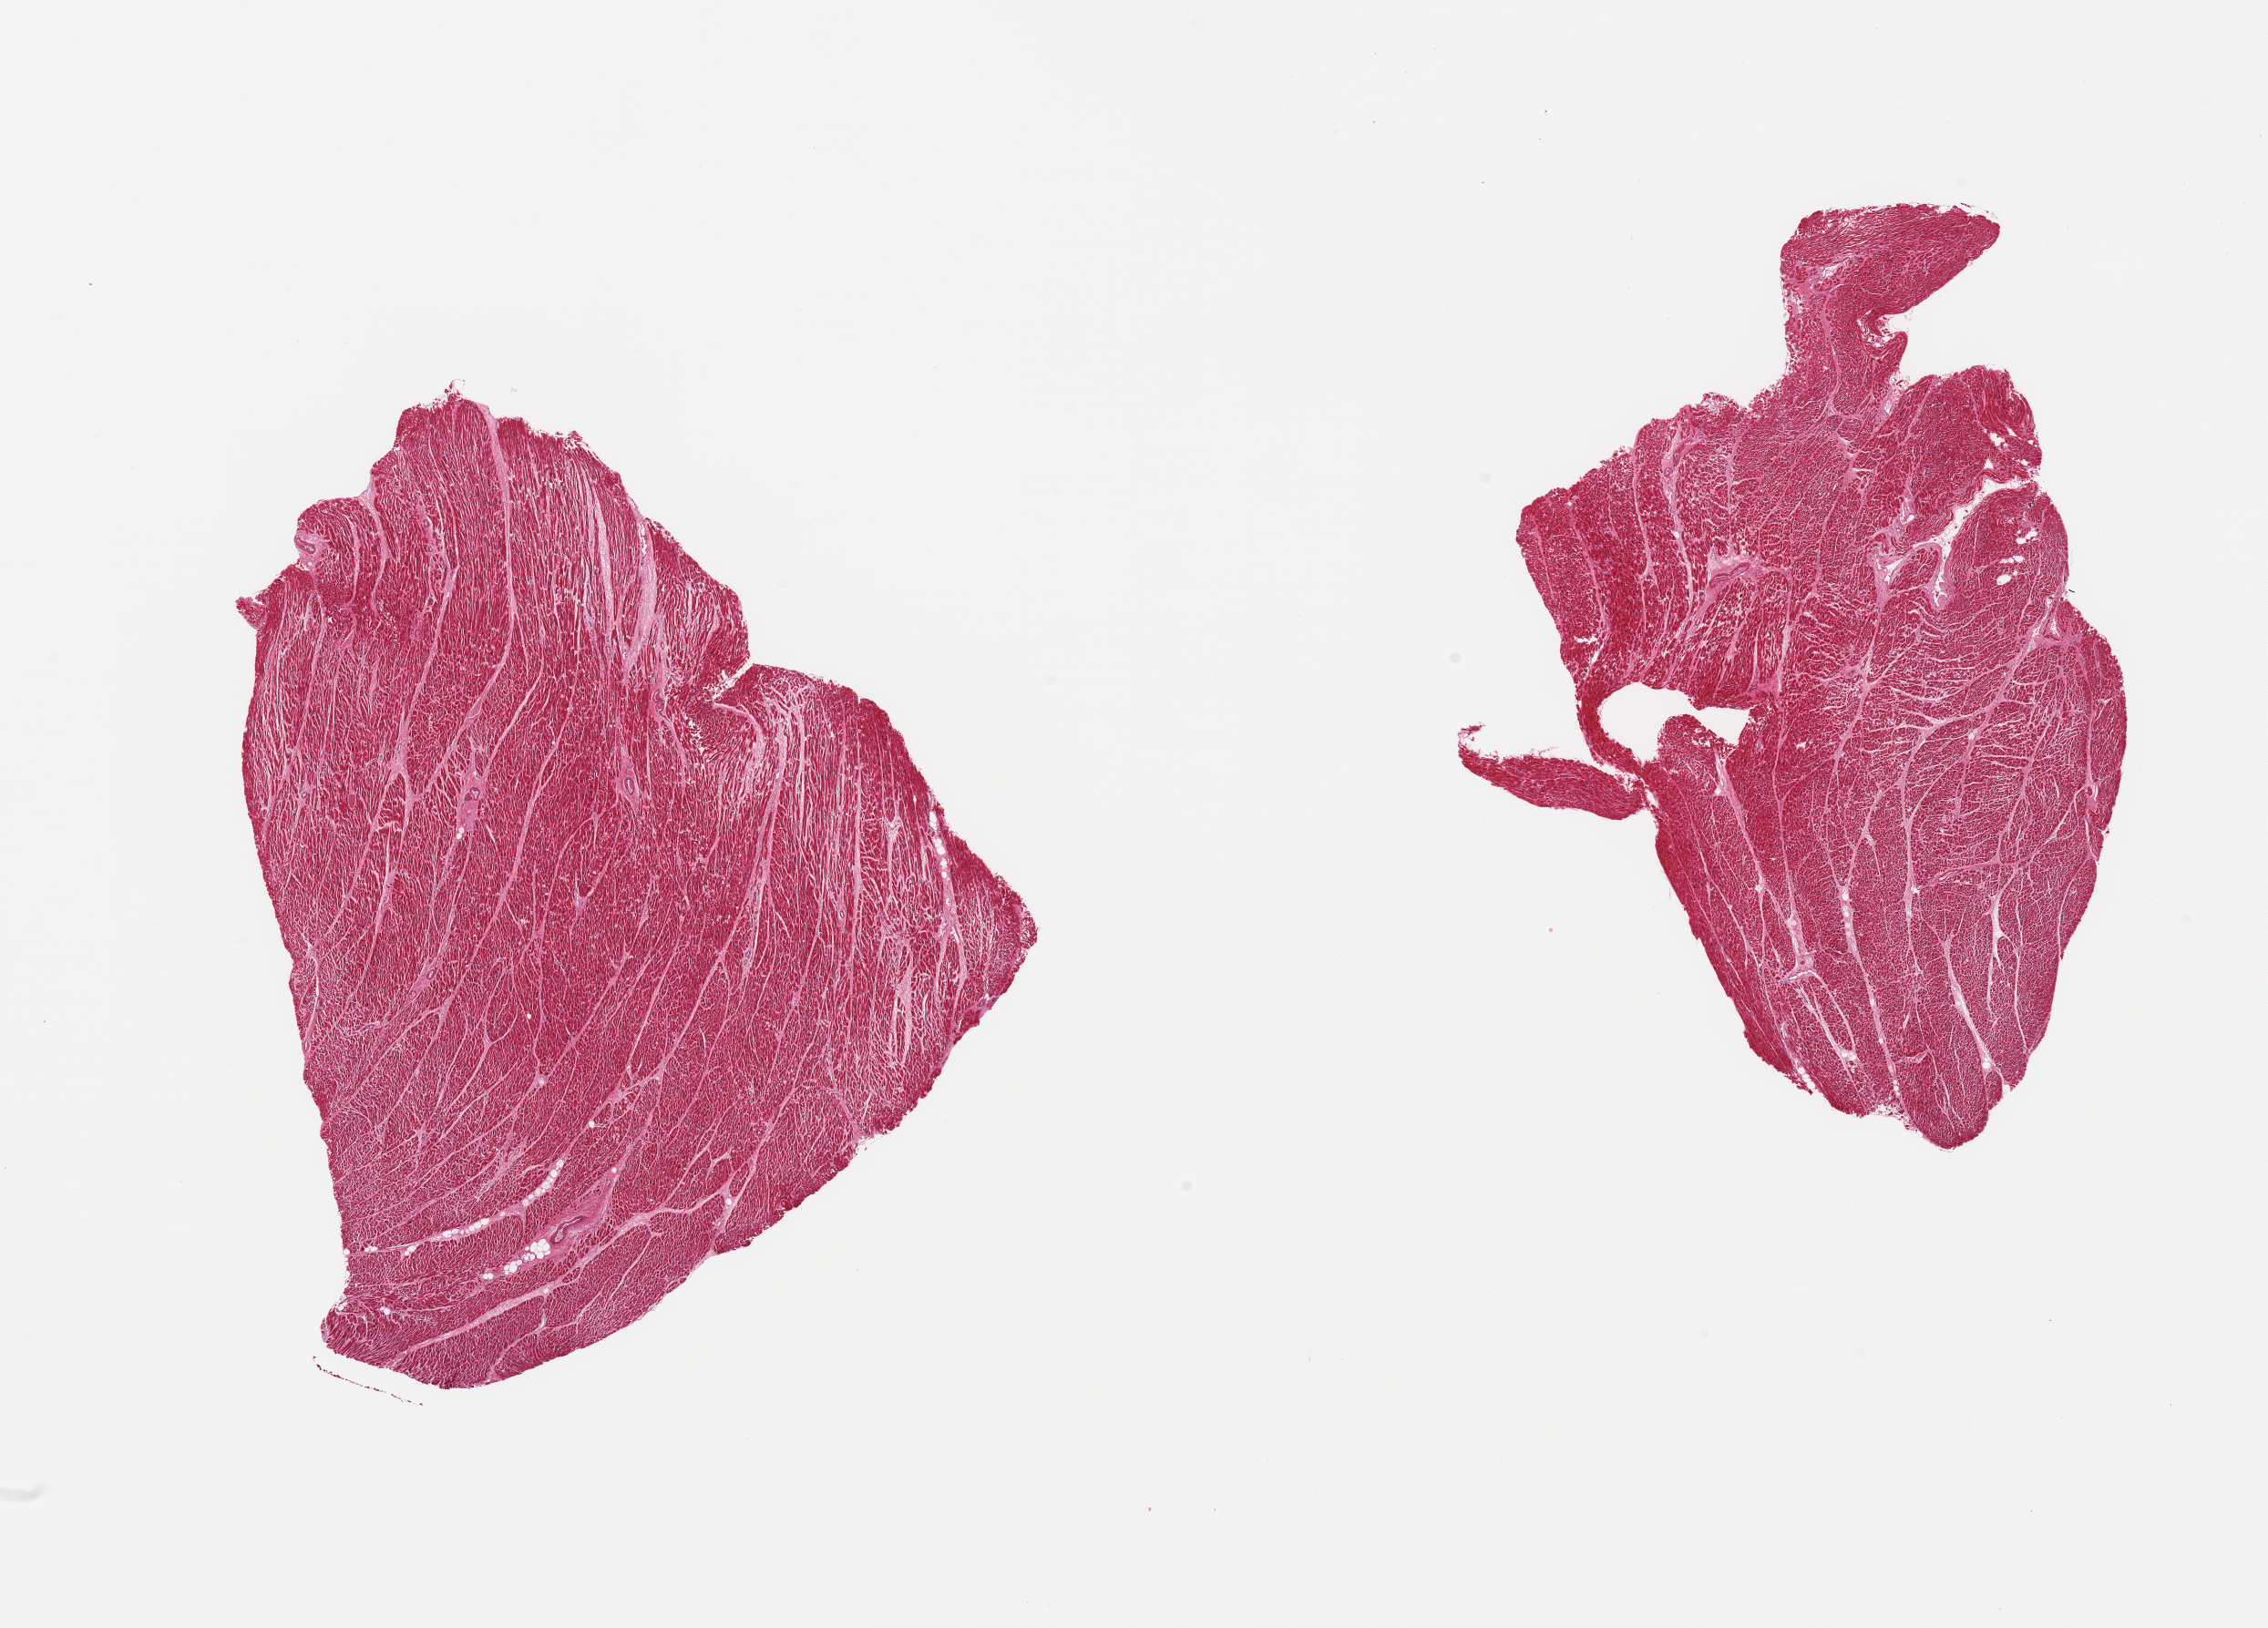
H&E whole-slide image, whole scanned area (about 19.7 x 14.1 mm, from a 20x scan) shown as a low-resolution overview, PAXgene-fixed, paraffin-embedded tissue, target tissue: heart, tissue donor sample. Female donor.
Reviewer comment on this tissue sample: 2 pieces; no sign of acute or chronic lesions.